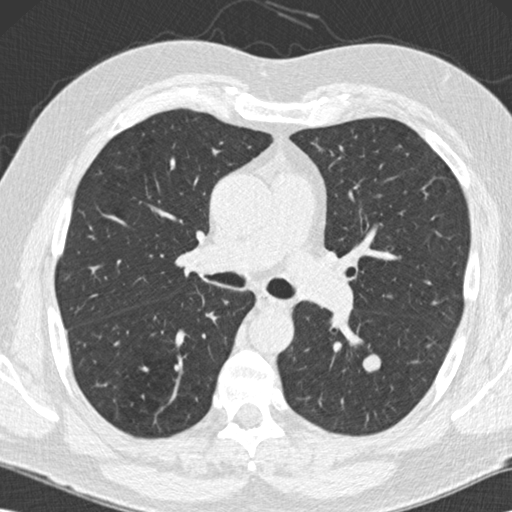
Low-dose screening chest CT, one axial slice. Position 87 of 152 along the scan axis. Reconstruction kernel B30f. Lung window (W 1500 / L -600 HU). 2 mm slice thickness. 512 × 512 image matrix, field of view 350 × 350 mm.
Outlined on this slice (expert manual segmentation):
- lesion 2 (nodule, lower lobe of left lung): bounding box <363,354,381,372> (left, top, right, bottom; pixels)